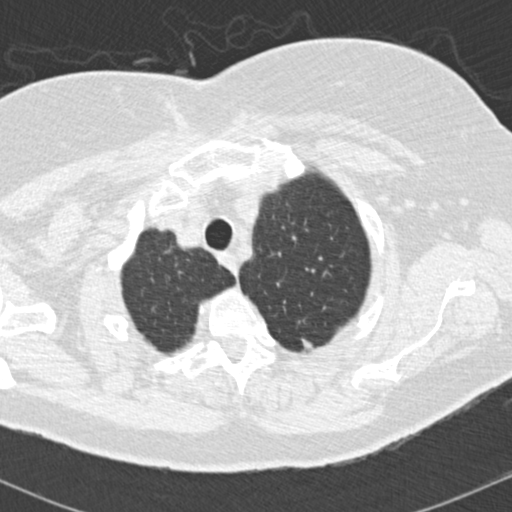
Low-dose screening chest CT, one axial slice. Slice 144 of 174 in the series (ordered by position). Reconstruction kernel B30f. Lung window (W 1500 / L -600 HU). 2 mm slice thickness. 512 × 512 image matrix, field of view 310 × 310 mm.
Structures marked on this image (outlined manually by an expert reader):
- lesion 1 (tumor, upper lobe of left lung): box from (x=301, y=336) to (x=314, y=353) px